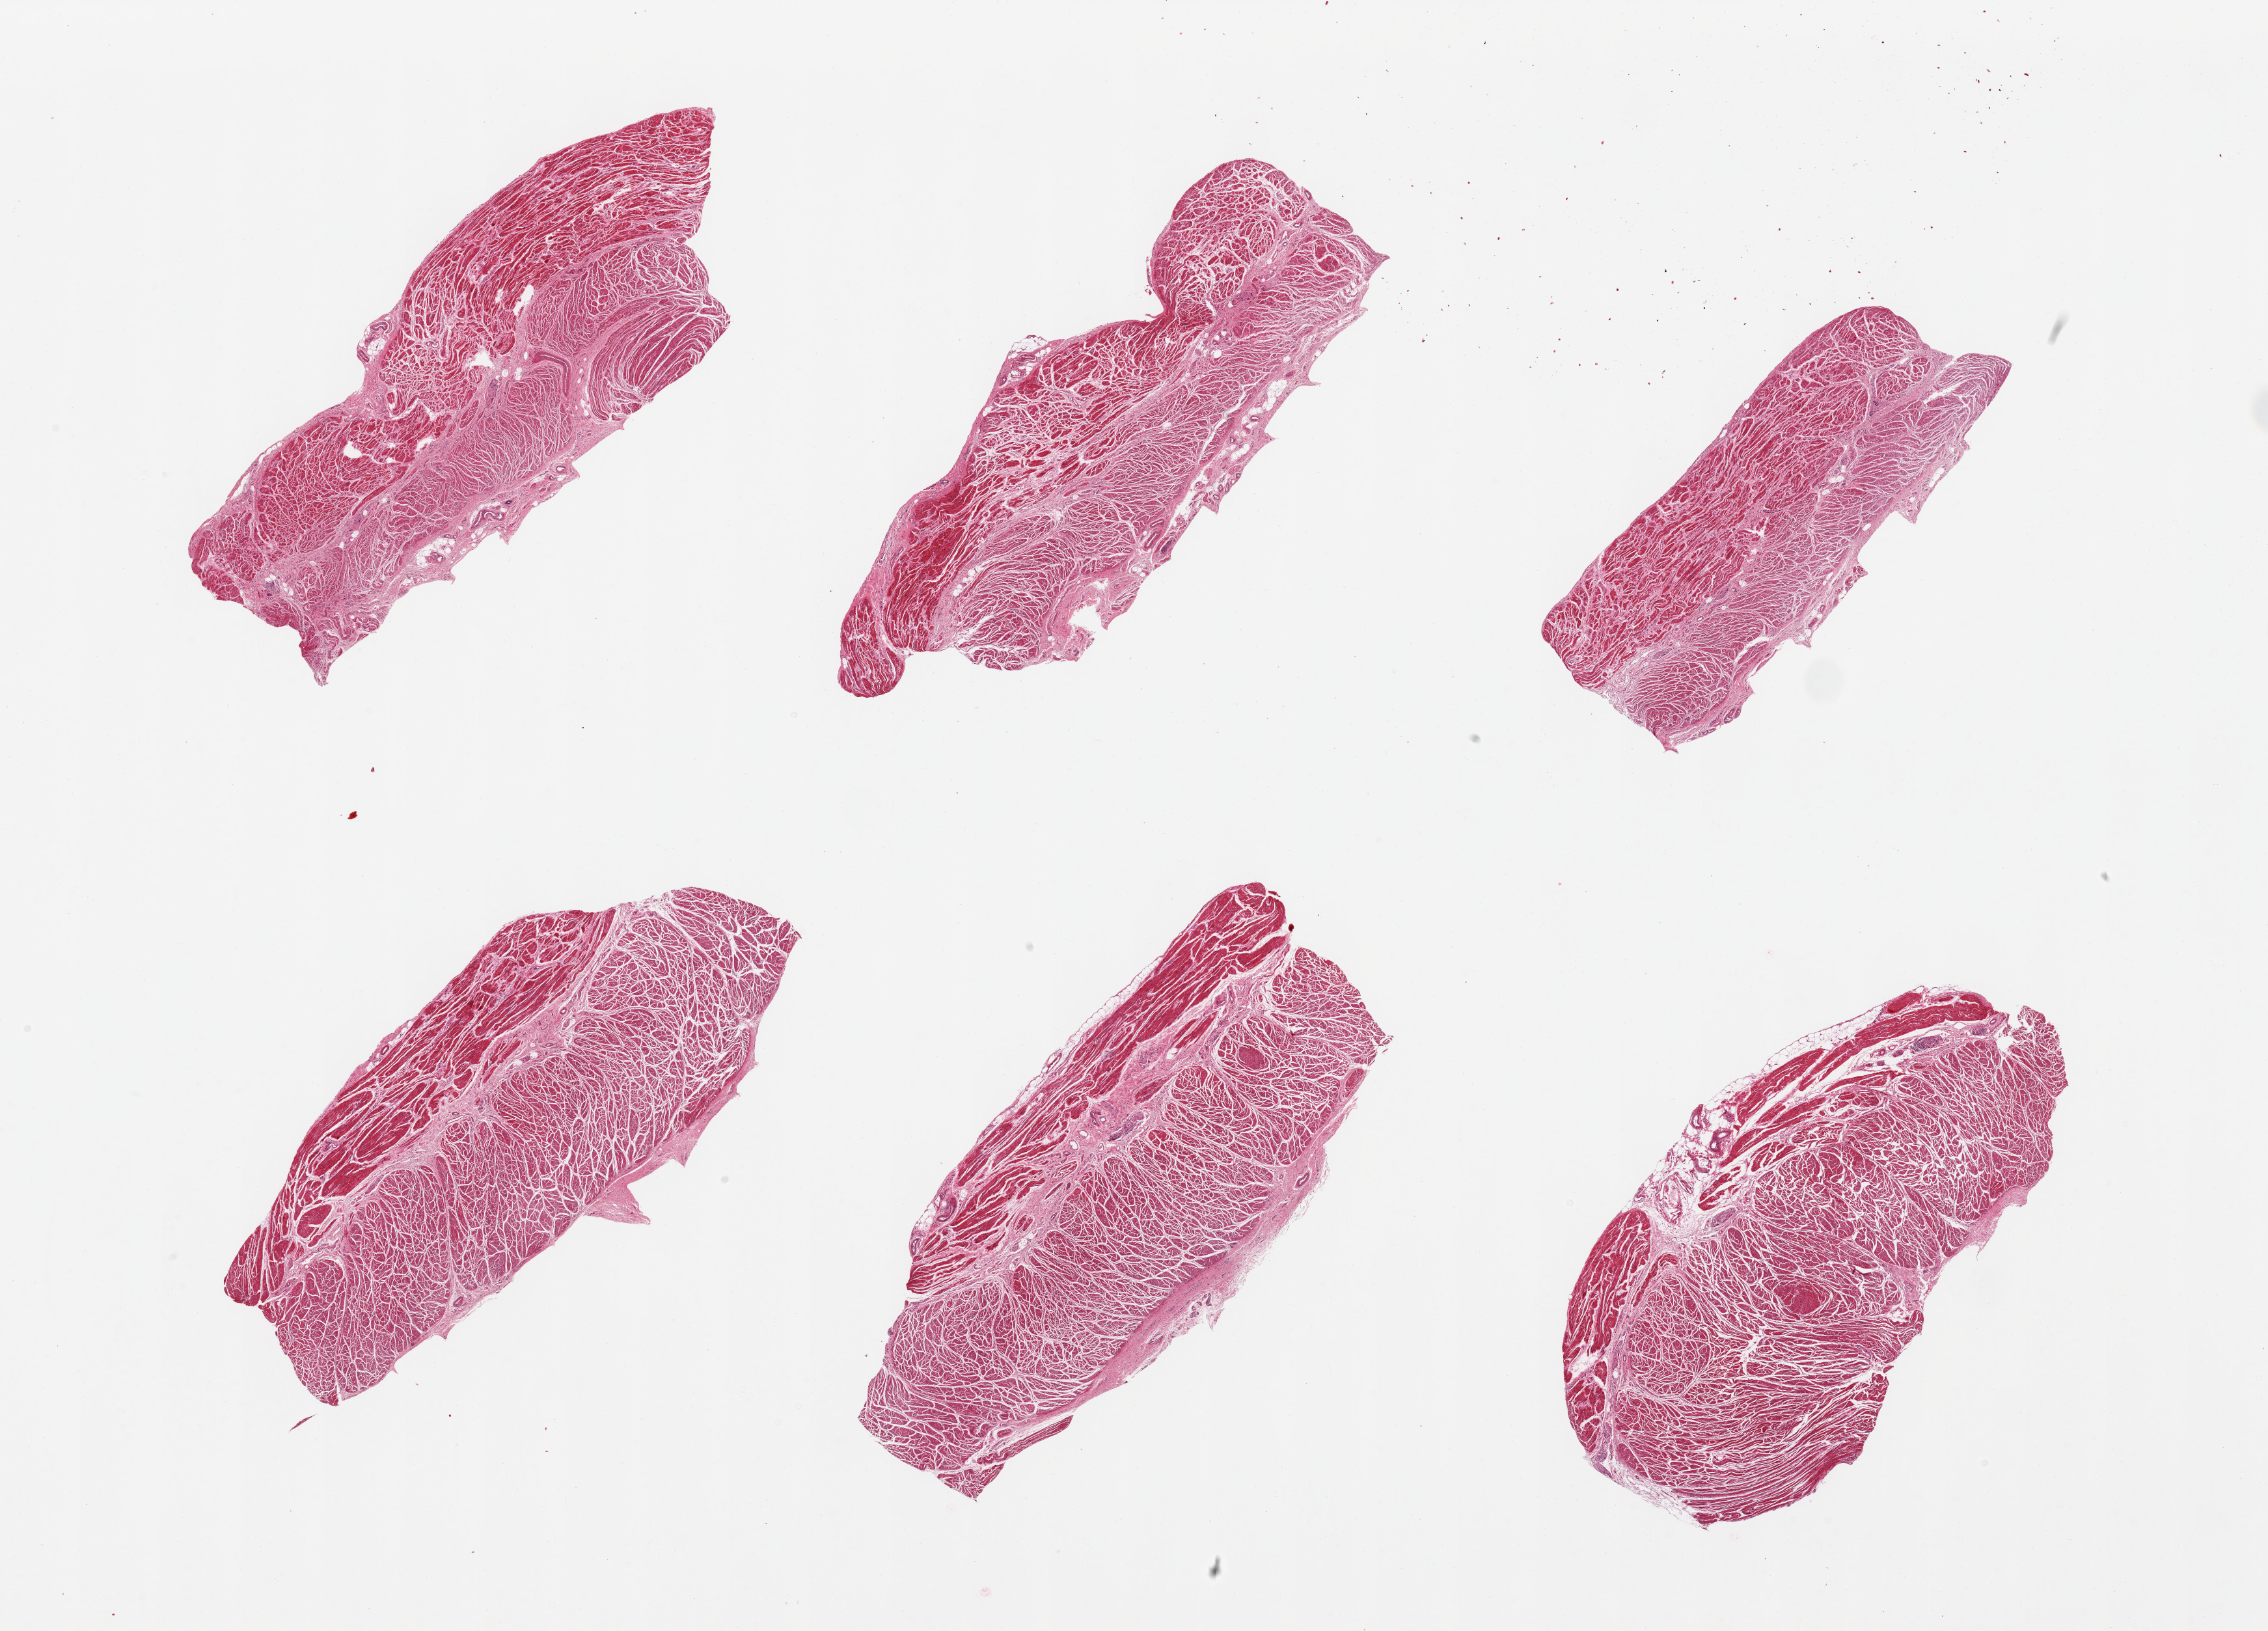
Whole-slide image, haematoxylin and eosin stain — a low-resolution overview of the entire scanned area, about 27.6 x 19.8 mm (acquisition: 20x scan). PAXgene-fixed paraffin-embedded (PFPE) section. Target tissue: gastroesophageal junction. Donor tissue sample. Female donor.
* reviewer comment on this tissue sample: 6 pieces; well dissected